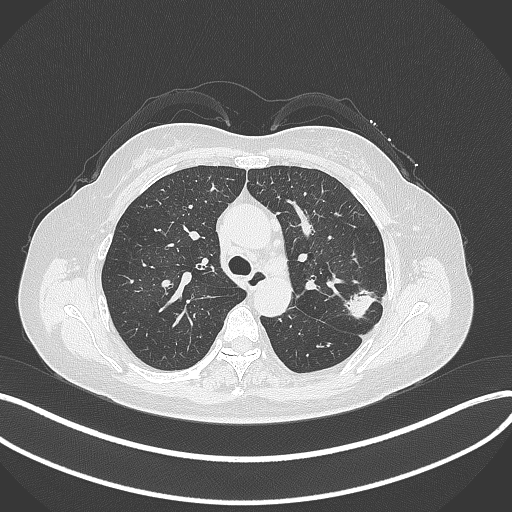
Chest CT, one axial slice. Position 223 of 319 along the scan axis. Lung window (W 1500 / L -600 HU). 1 mm slice thickness. 512 × 512 image matrix. Patient: female, 60 years. Case-level facts recorded for this patient, not image findings: clinical TNM (as recorded): T1c N0 M0.
Structures marked on this image (bounding box drawn by a radiologist):
- lung tumour (recorded histology: adenocarcinoma): bounding box [x1, y1, x2, y2] px = [340, 287, 378, 322]